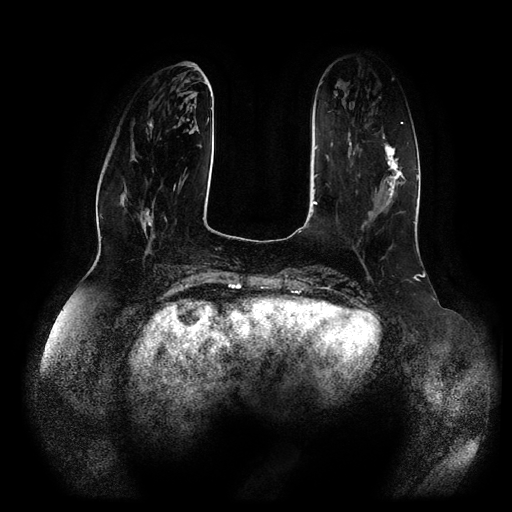
Breast MRI (dynamic contrast-enhanced, multi-phase), one axial slice; position 30 of 116 along the scan axis; dynamic contrast-enhanced series, time point 2 of 5 at this slice position (early post-contrast); 1.5 T; TE 2.5 ms, TR 5.2 ms; 512 × 512 image matrix, field of view 400 × 400 mm. Female patient, age 66 years.
Outlined on this slice (semi-automatically segmented with operator editing):
- breast lesion (labelled 'tumour' in the annotation; benign lesions carry a separate 'benign' label): bounding box <383,134,406,206> (left, top, right, bottom; pixels)